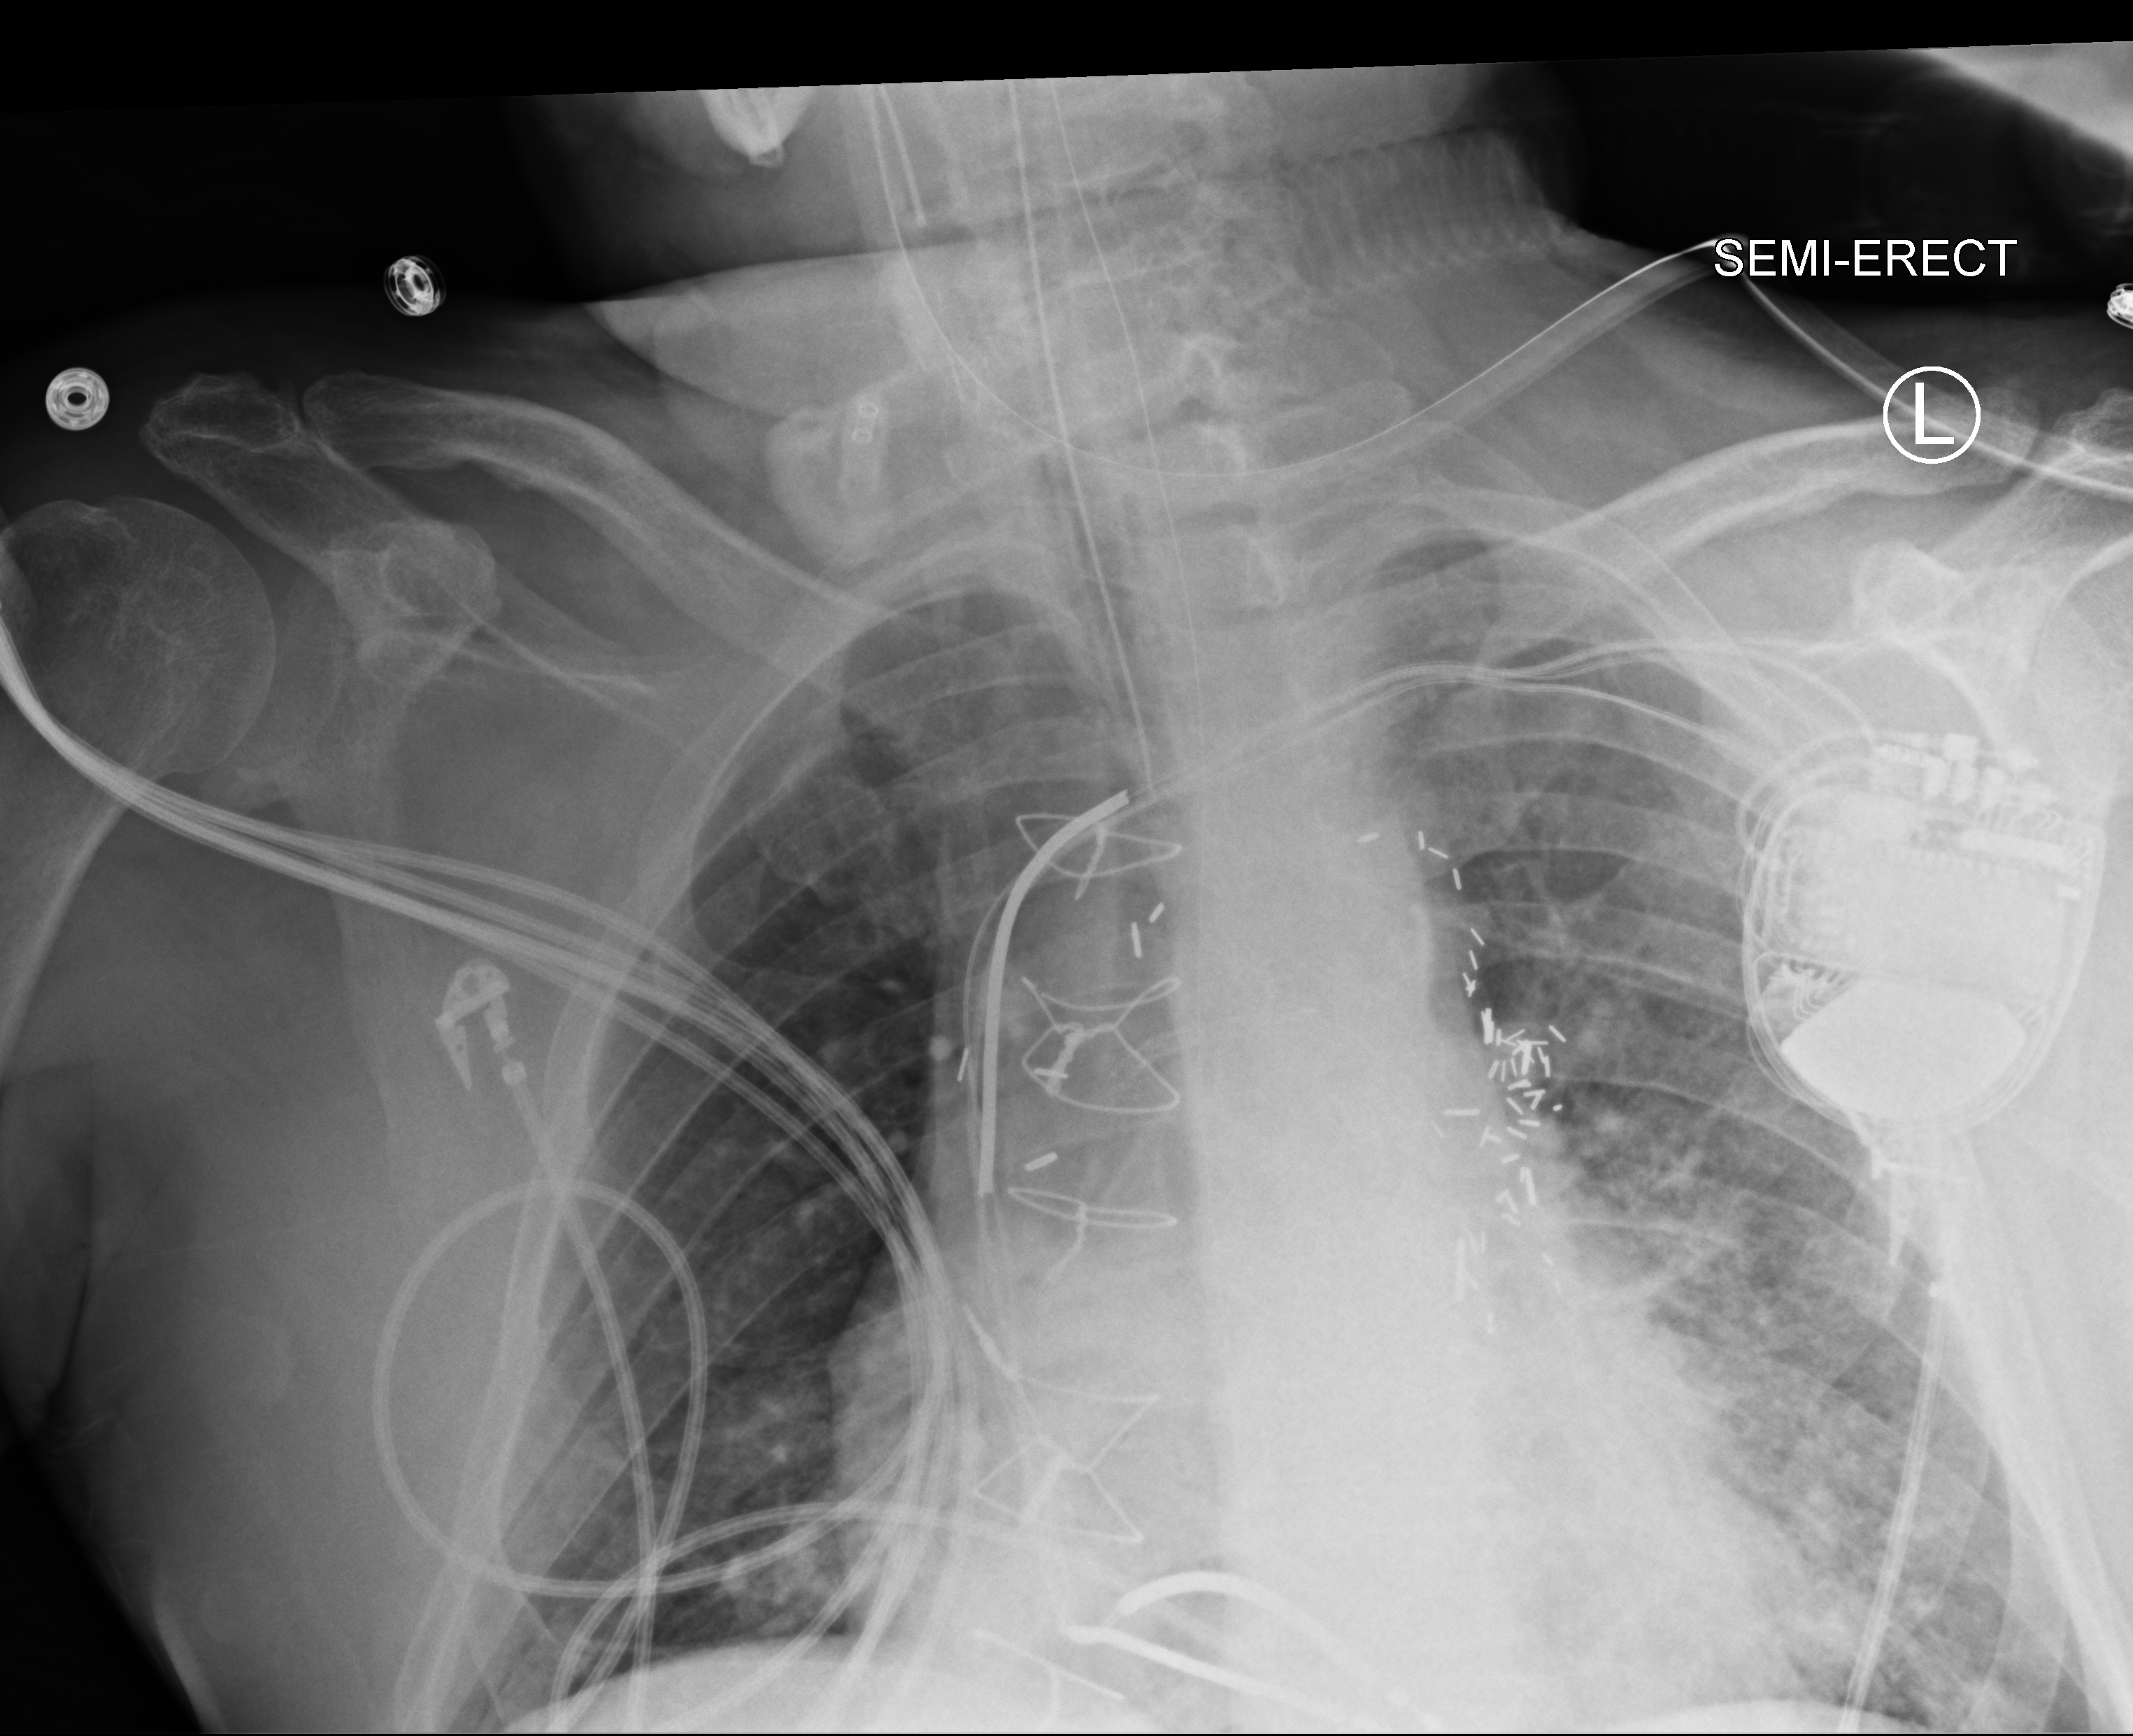
Chest X-ray (portable), anteroposterior (AP) projection. Patient hospitalised with COVID-19; male, aged 60–74 years.
From the hospital-stay record, not from the radiograph (when in the stay this image was taken is not recorded):
- admitted to intensive care during this hospital stay: yes
- chronic kidney disease (admission record): no
- mechanically ventilated during this hospital stay: yes